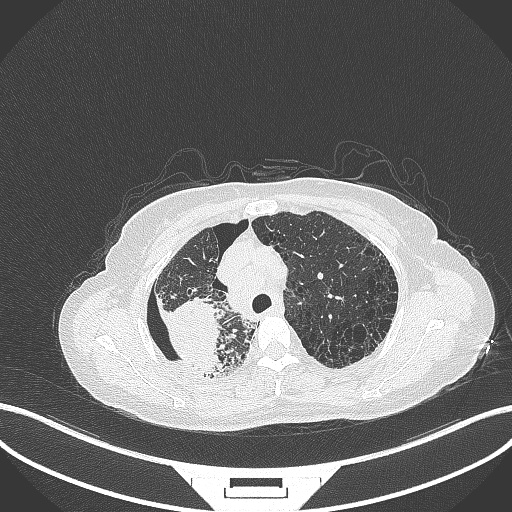
Chest CT, one axial slice. Position 269 of 408 along the scan axis. Reconstruction kernel B70f. Lung window (W 1500 / L -600 HU). 1 mm slice thickness. 512 × 512 image matrix, field of view 400 × 400 mm. Patient: female, 64 years. Case-level facts recorded for this patient, not image findings: clinical TNM (as recorded): T3 N3 M0.
Structures marked on this image (bounding box drawn by a radiologist):
- lung tumour (recorded histology: squamous cell carcinoma): bounding box (x1, y1, x2, y2) in pixels: (155, 291, 226, 372)